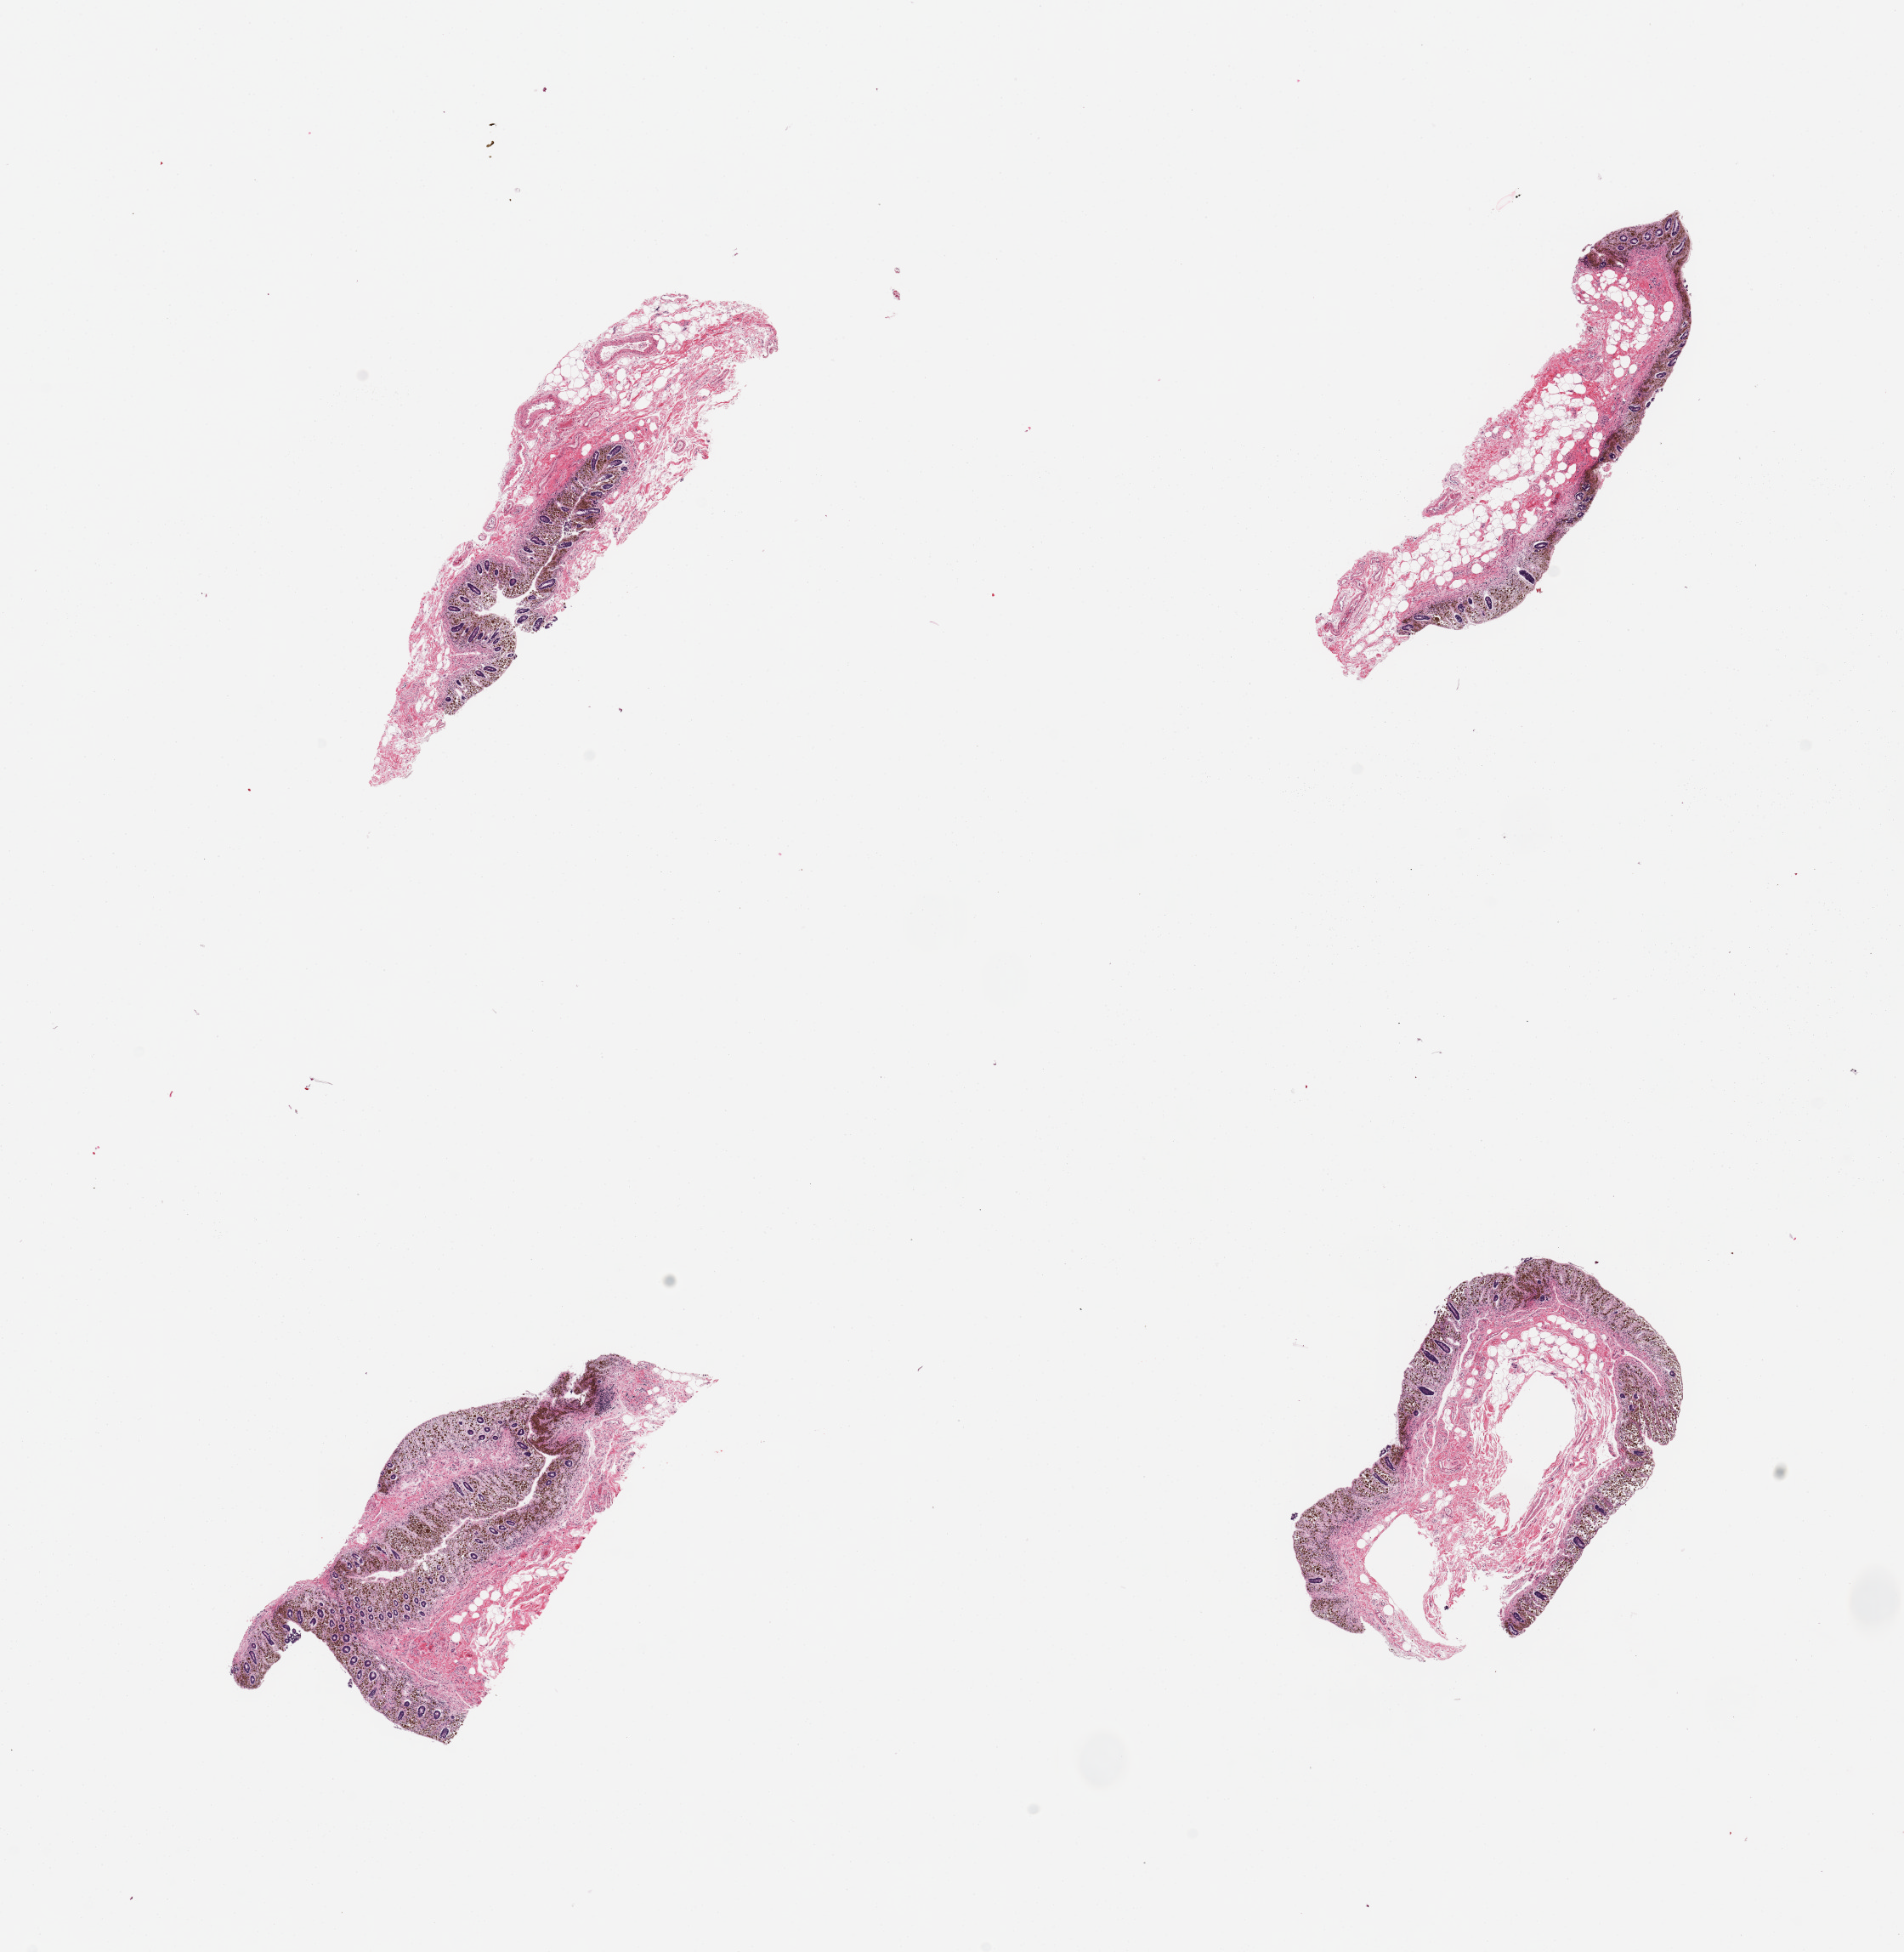
Whole-slide image, H&E stain, low-resolution overview of the scanned area, about 17.7 x 18.2 mm. Donor sex: male.
Specimen: PAXgene-fixed, paraffin-embedded tissue; section of transverse colon (target tissue); tissue donor sample.